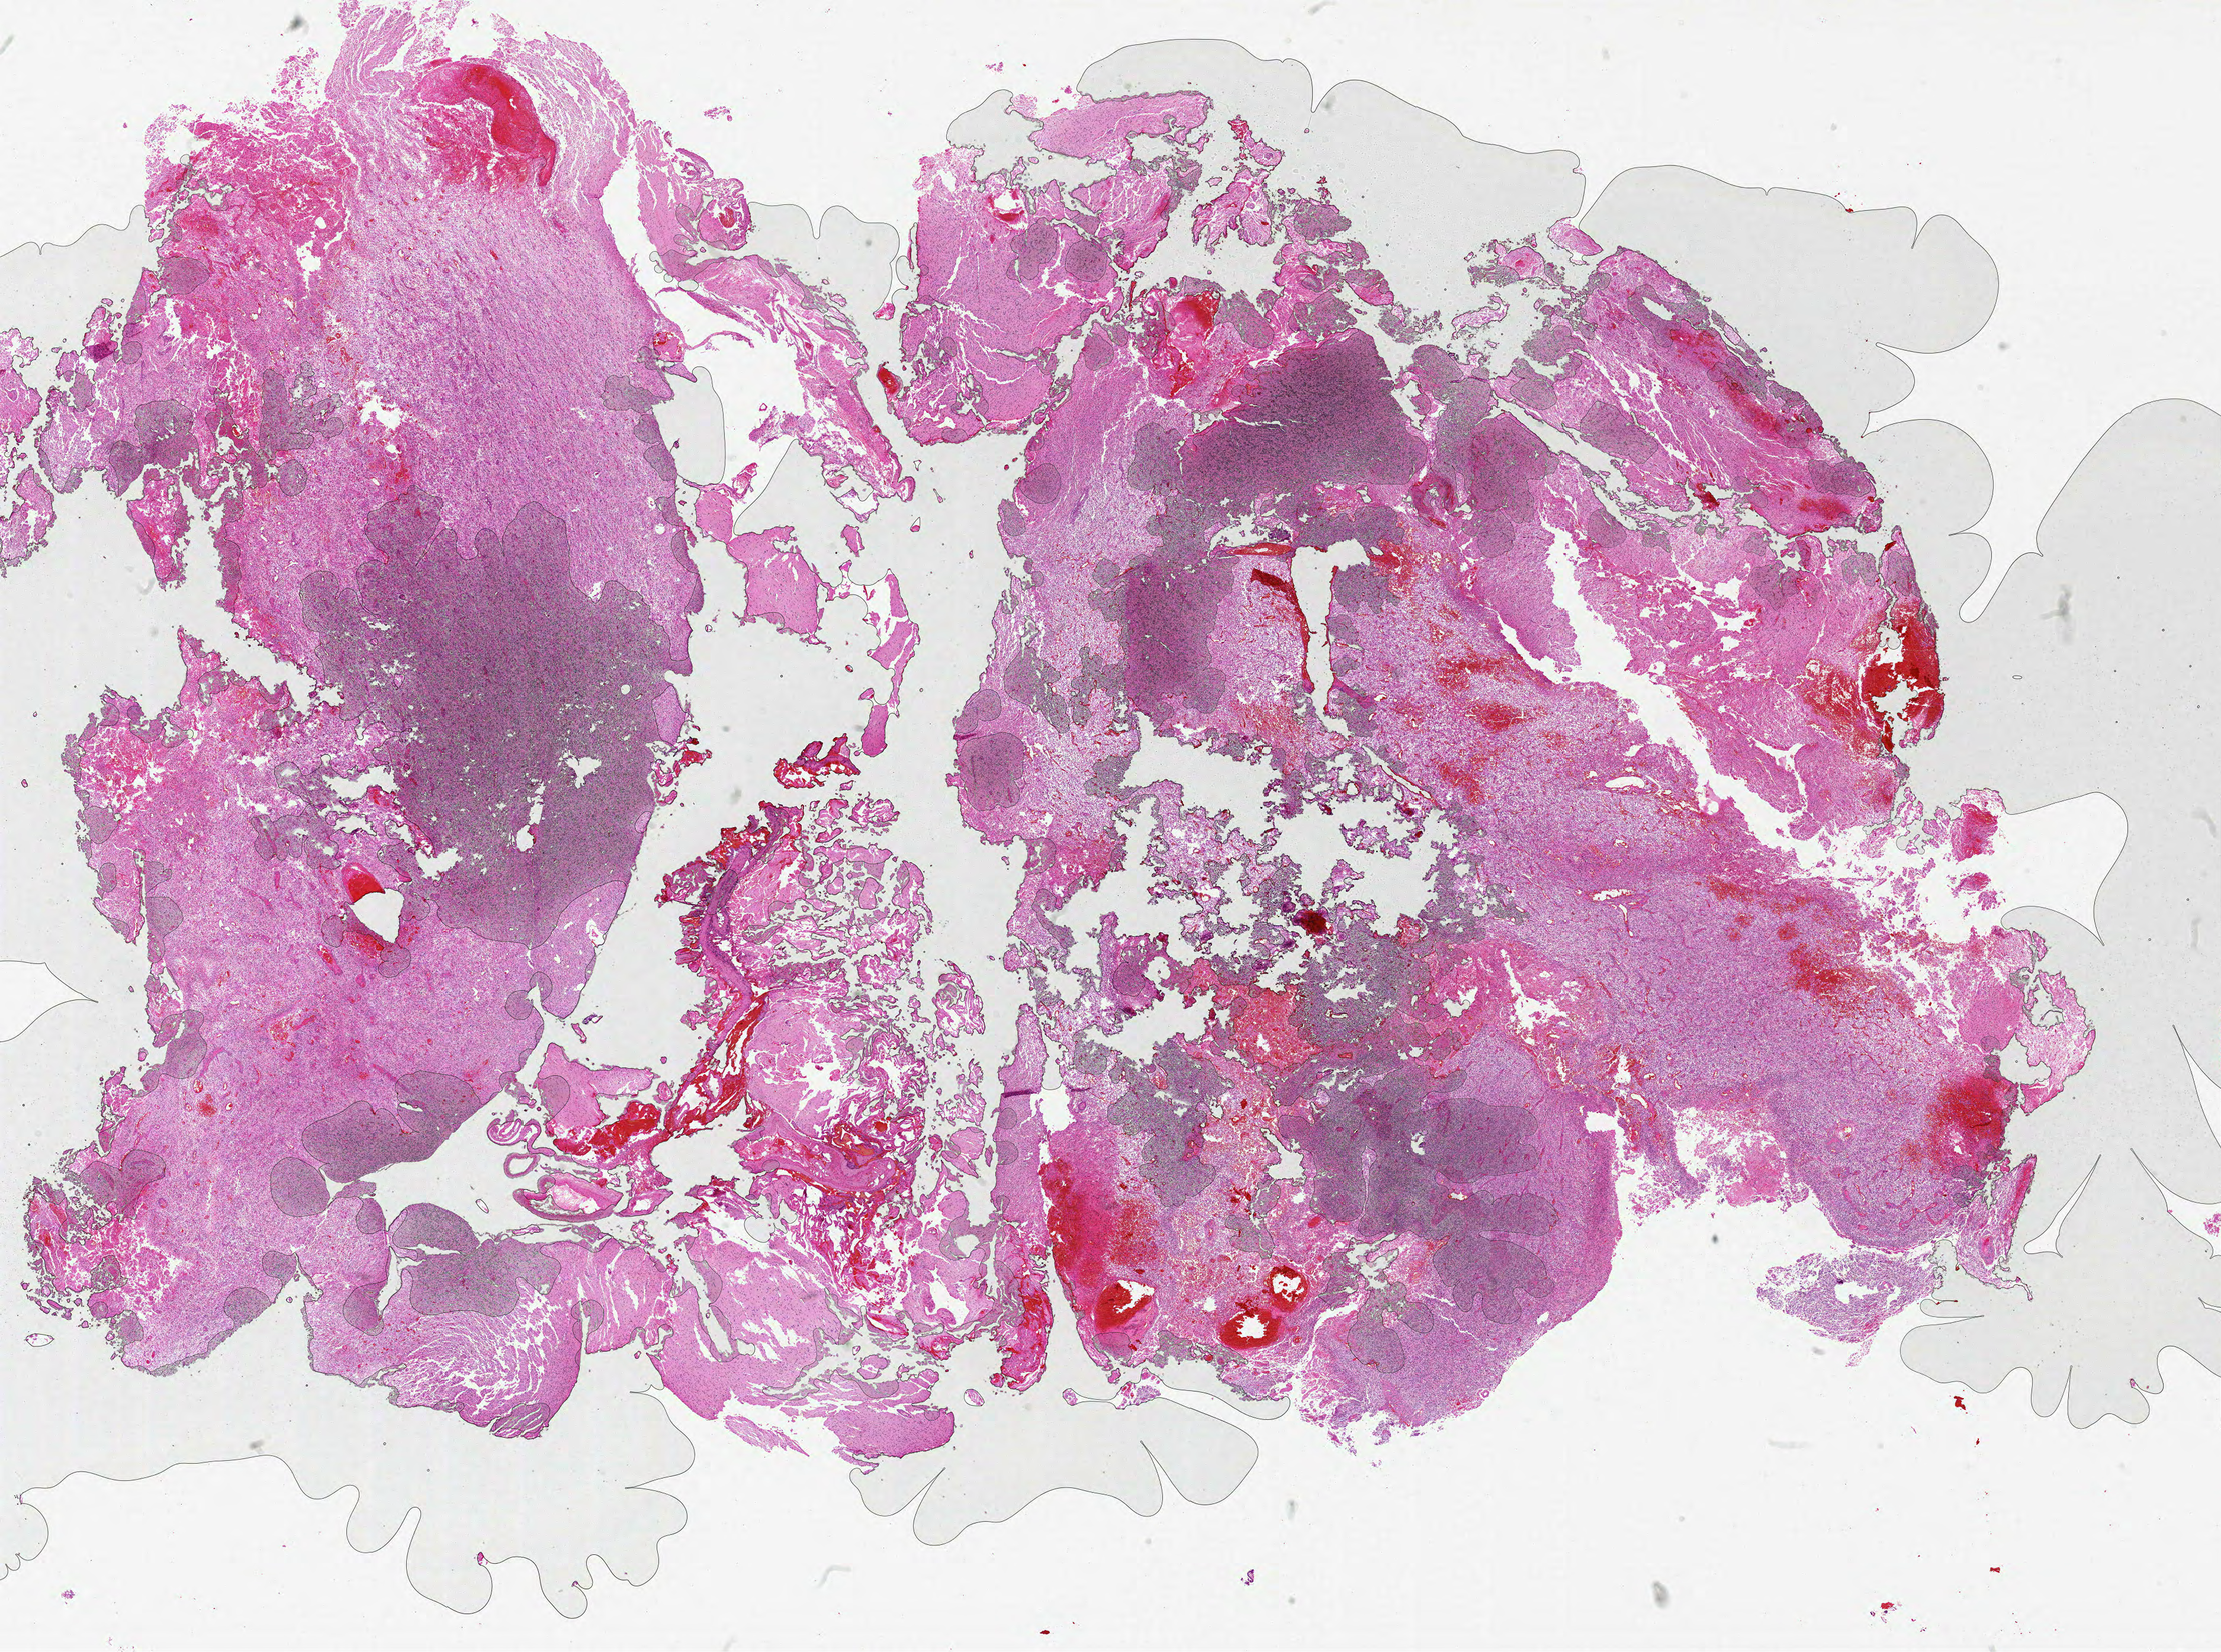
Hematoxylin and eosin (H&E) stained whole-slide image — whole scanned area (about 30.0 x 22.3 mm, slide scanned at 20x) shown as a low-resolution overview, FFPE section, sample: primary tumour, brain. Male, age 53 years at initial diagnosis.
* histologic diagnosis: Glioblastoma